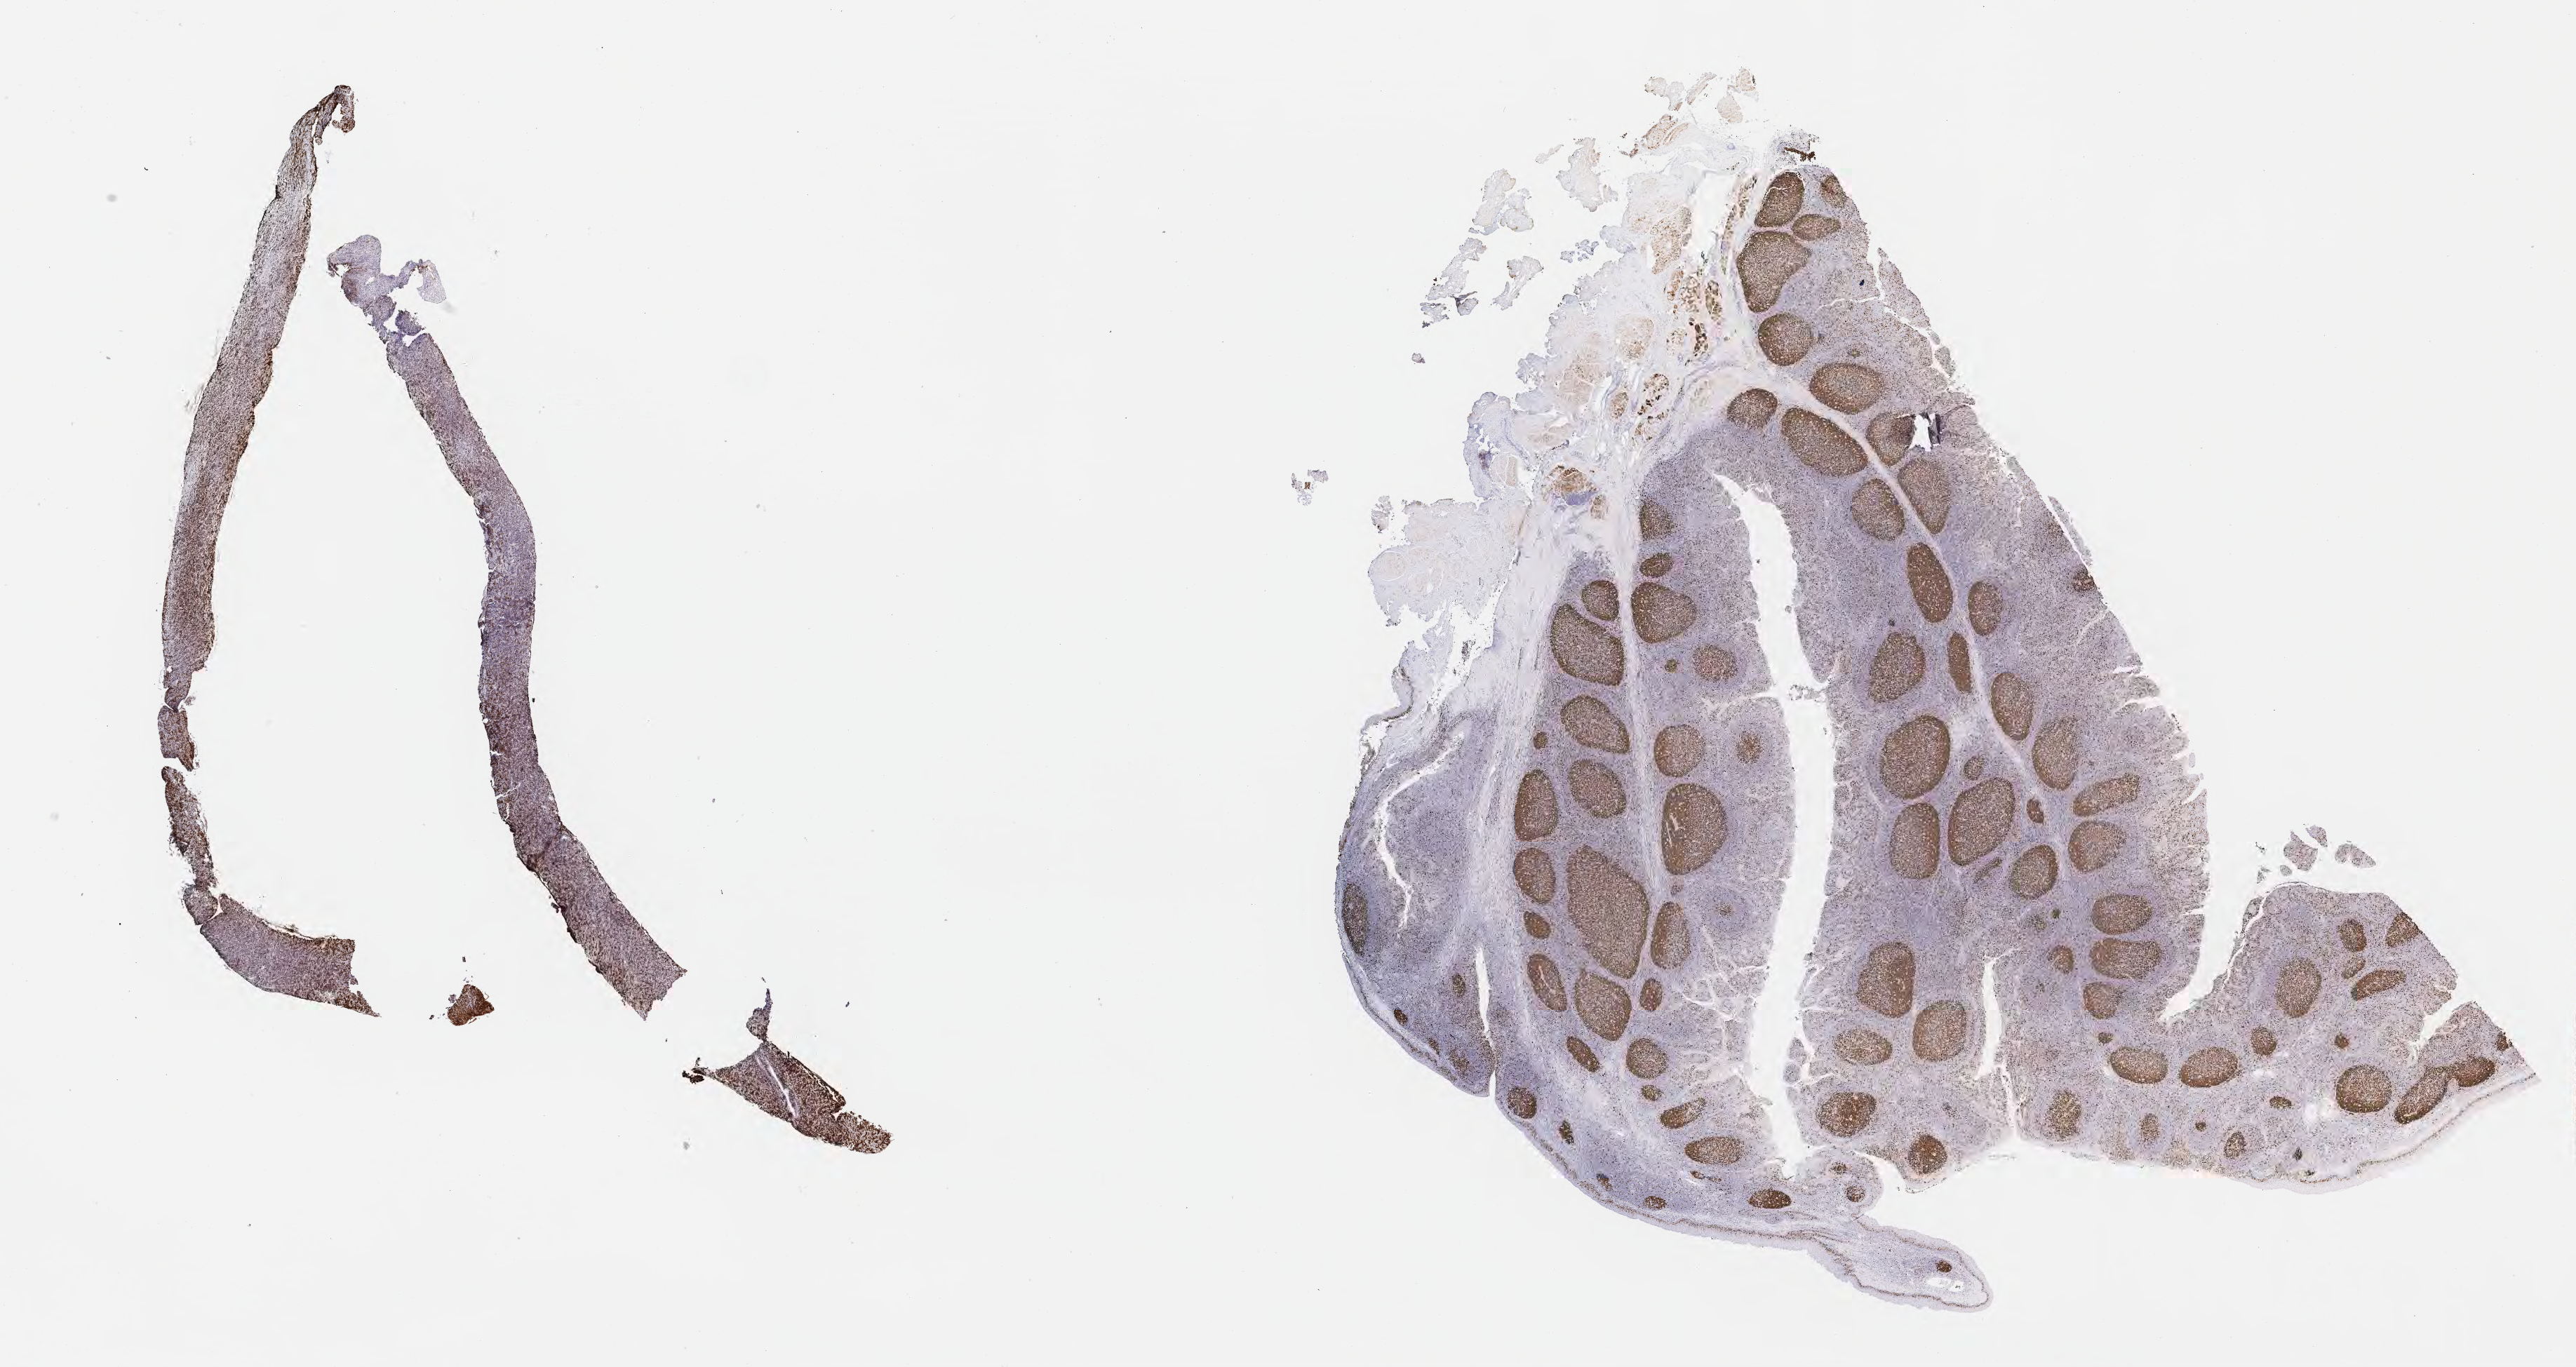
Whole-slide image, immunohistochemical stain for Ki-67, a low-resolution overview of the entire scanned area, about 29.7 x 15.8 mm; tumor tissue; anatomic site: abdomen proper. Patient: male, age at initial diagnosis 9 years.
Diagnosis: Burkitt lymphoma, NOS.